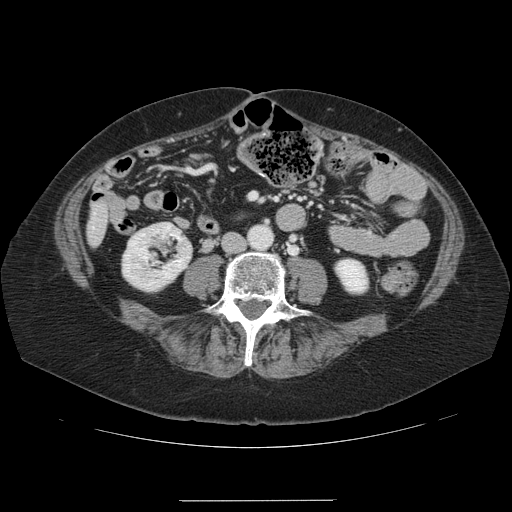
Contrast-enhanced abdominal CT, one axial slice; slice 12 of 141 in the series (ordered by position); 120 kVp; intravenous contrast given; soft-tissue window (W 400 / L 40 HU); 2.5 mm slice thickness; 512 × 512 image matrix, field of view 393 × 393 mm. Female patient, age 74 years. From the clinical record (not read from this slice): diagnosis: colorectal cancer liver metastases, imaged before liver resection; multiple liver metastases: yes; largest metastasis: 7 cm.
Outlined on this slice (outlined manually by an expert reader):
- liver: bounding box (x1, y1, x2, y2) in pixels: (88, 203, 108, 244)
- planned liver remnant (the part of the liver to remain after resection): (91, 203, 108, 244)